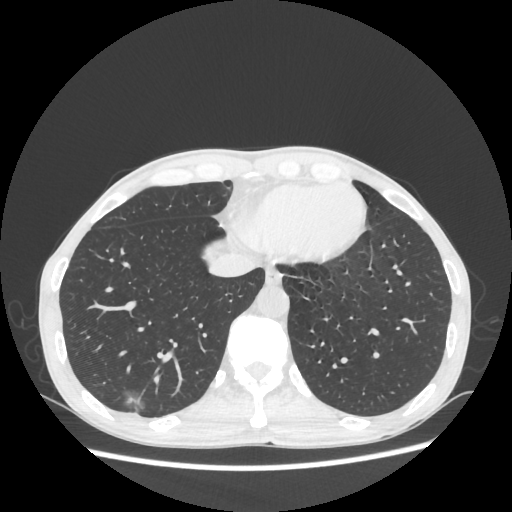
Chest CT, one axial slice; slice 73 of 270 in the series (ordered by position); reconstruction kernel STANDARD; 100 kVp; lung window (W 1500 / L -600 HU); 512 × 512 image matrix. Male patient, age 60 years. Case-level facts recorded for this patient, not image findings: clinical TNM (as recorded): T1c N0 M0.
Annotated regions visible in this slice (bounding box drawn by a radiologist):
- lung tumour (recorded histology: adenocarcinoma): box from (x=117, y=385) to (x=158, y=427) px